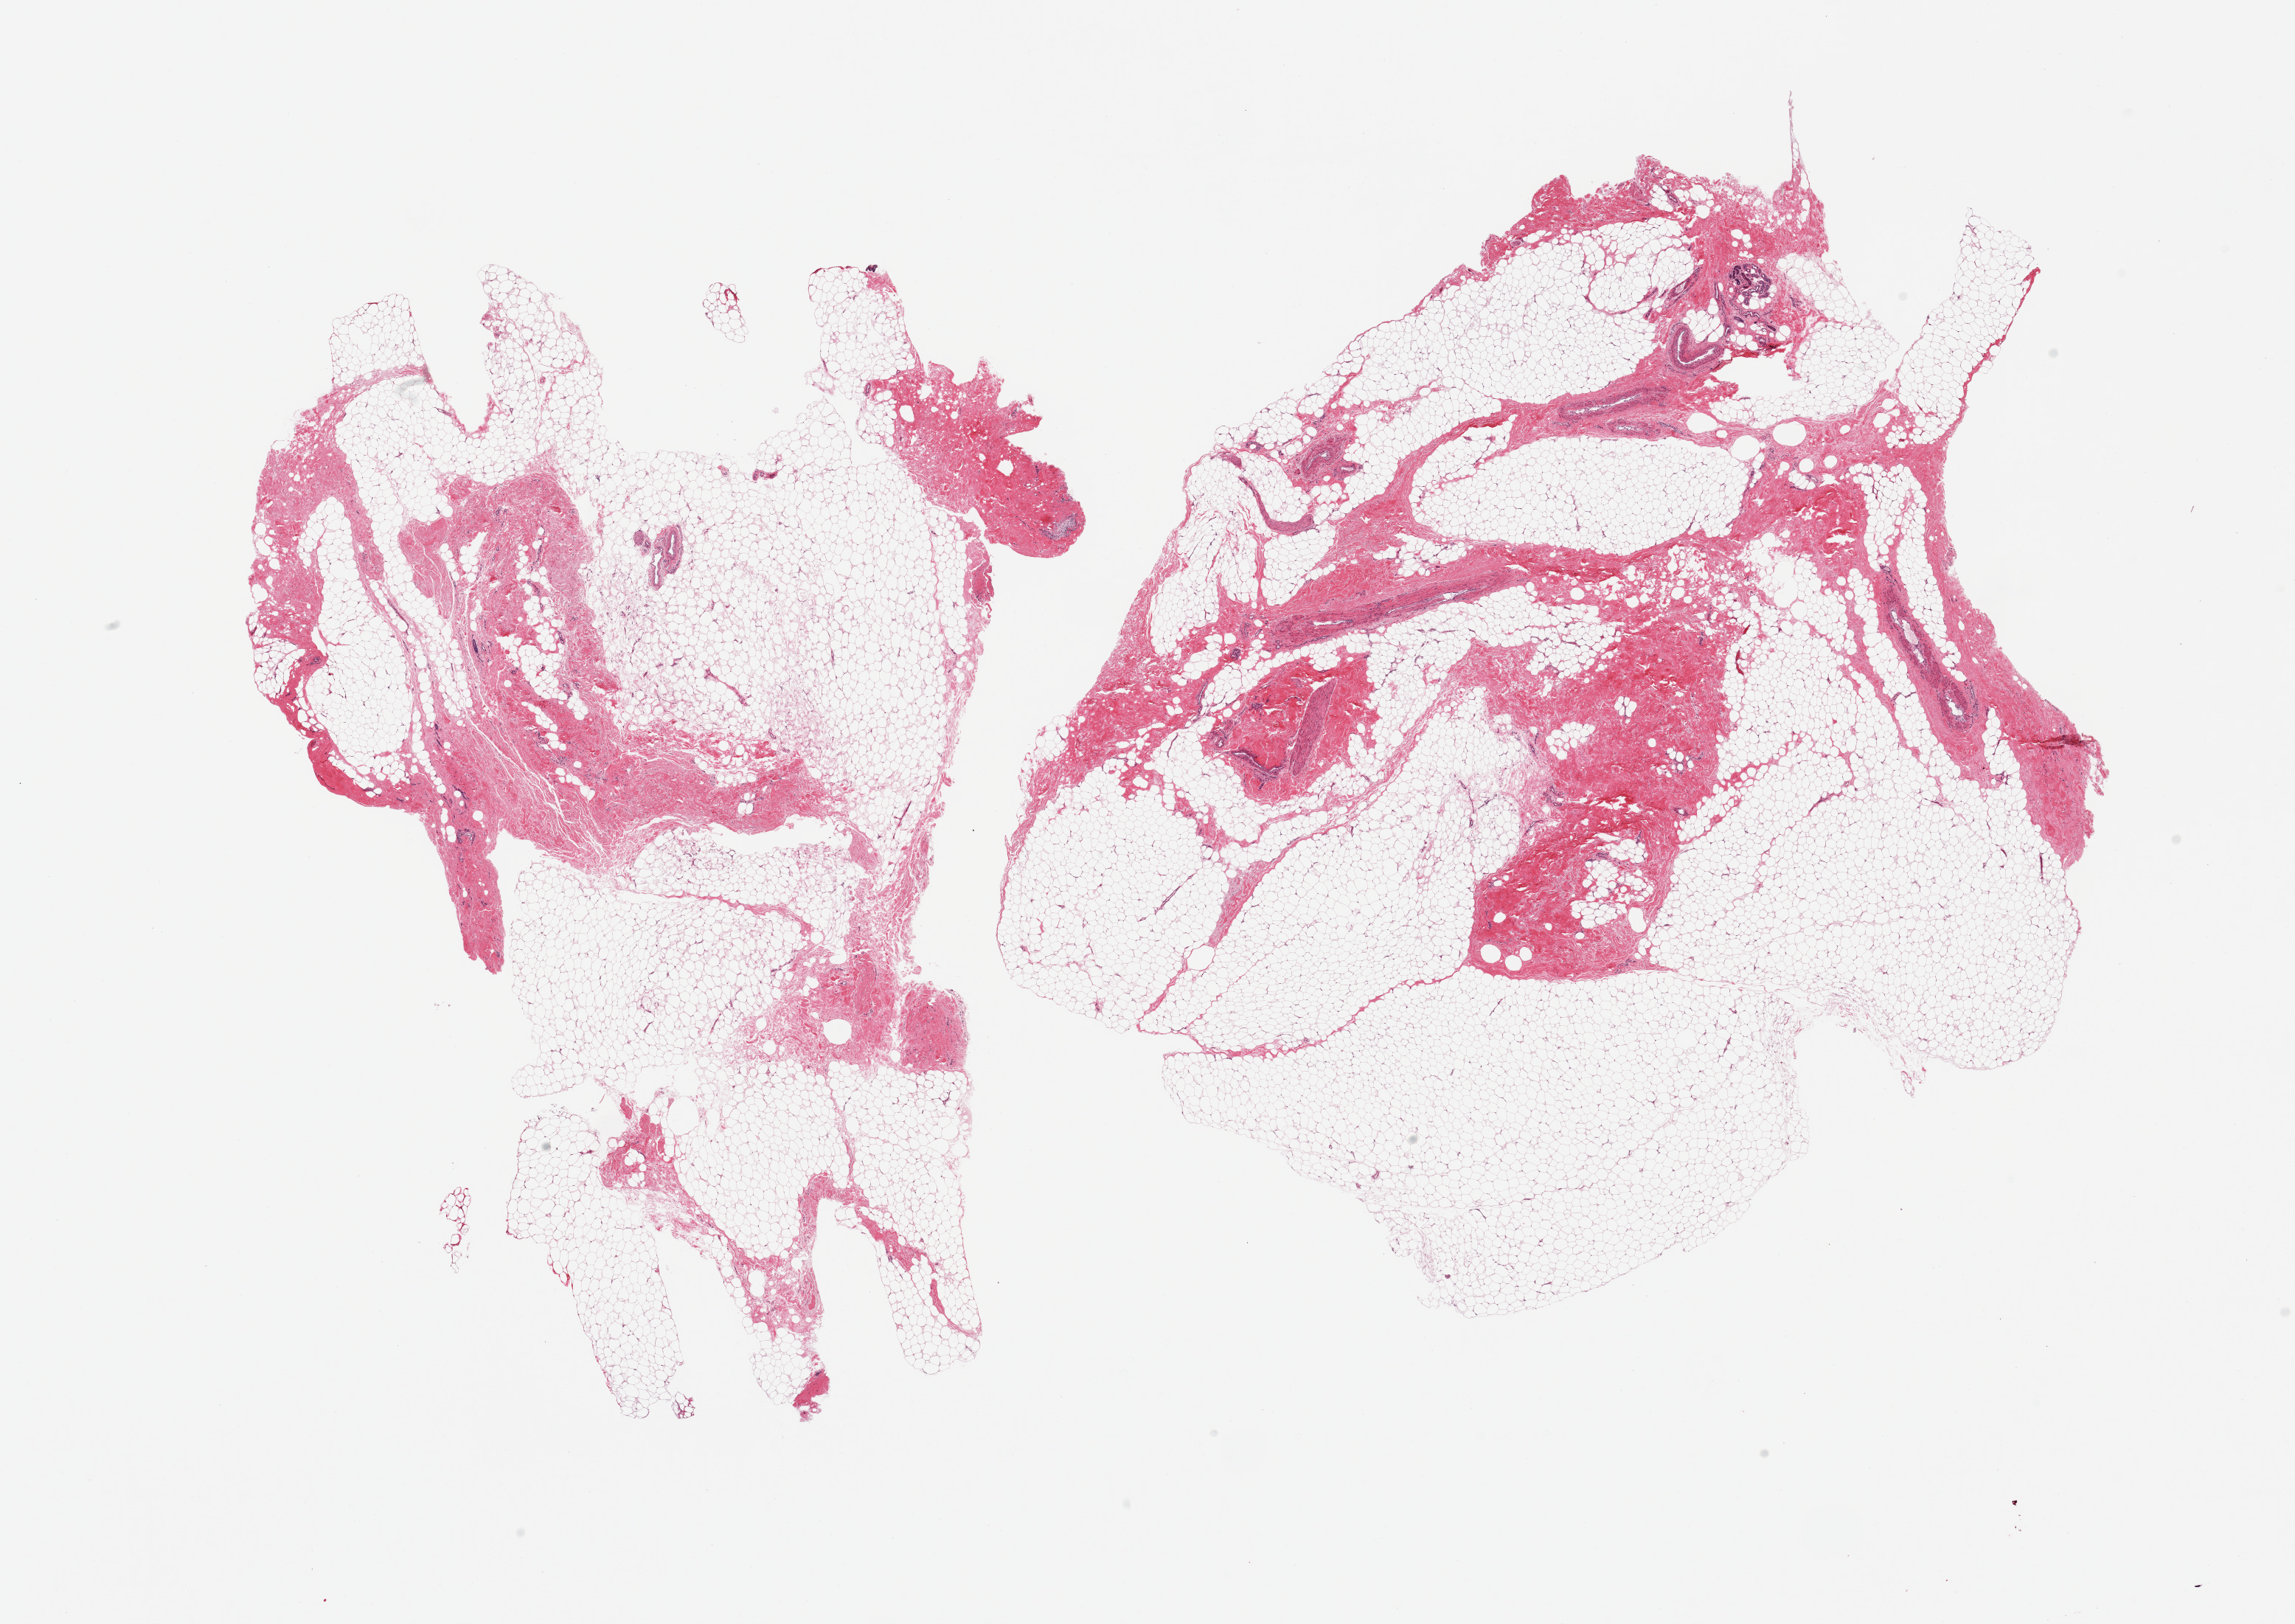
H&E whole-slide image, brightfield, a low-resolution overview of the entire scanned area, about 24.6 x 17.4 mm (acquisition: 20x scan). PAXgene-fixed paraffin-embedded (PFPE) section. Sampled site (target tissue): breast. Tissue donor sample. Donor: female.
• pathologist's review note for this sample: 2 pieces, mainly fibroadipose tissue, few foci of TDLU